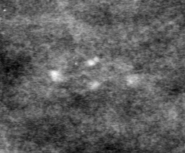
Region of interest cut from a scanned film mammogram (one marked finding), left breast, CC view, BI-RADS breast density category 2 (scale 1–4).
Finding: calcifications, morphology pleomorphic, distribution clustered; BI-RADS assessment category 4; pathology (as recorded): benign.